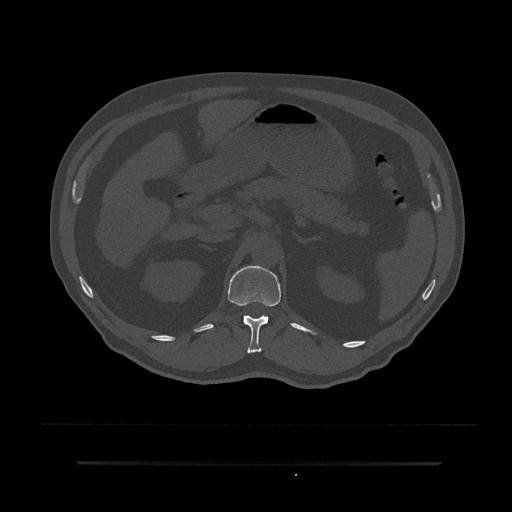
CT including the spine, one axial slice; position 195 of 797 along the scan axis; reconstruction kernel Br40s/3; bone window (W 1800 / L 400 HU); 512 × 512 image matrix, field of view 464 × 464 mm. Patient: male, 59 years. Case-level facts recorded for this patient, not image findings: primary cancer: bile ducts.
Annotated regions visible in this slice (semi-automatically segmented with operator editing):
- T12 vertebra: bounding box <228,265,281,354> (left, top, right, bottom; pixels)